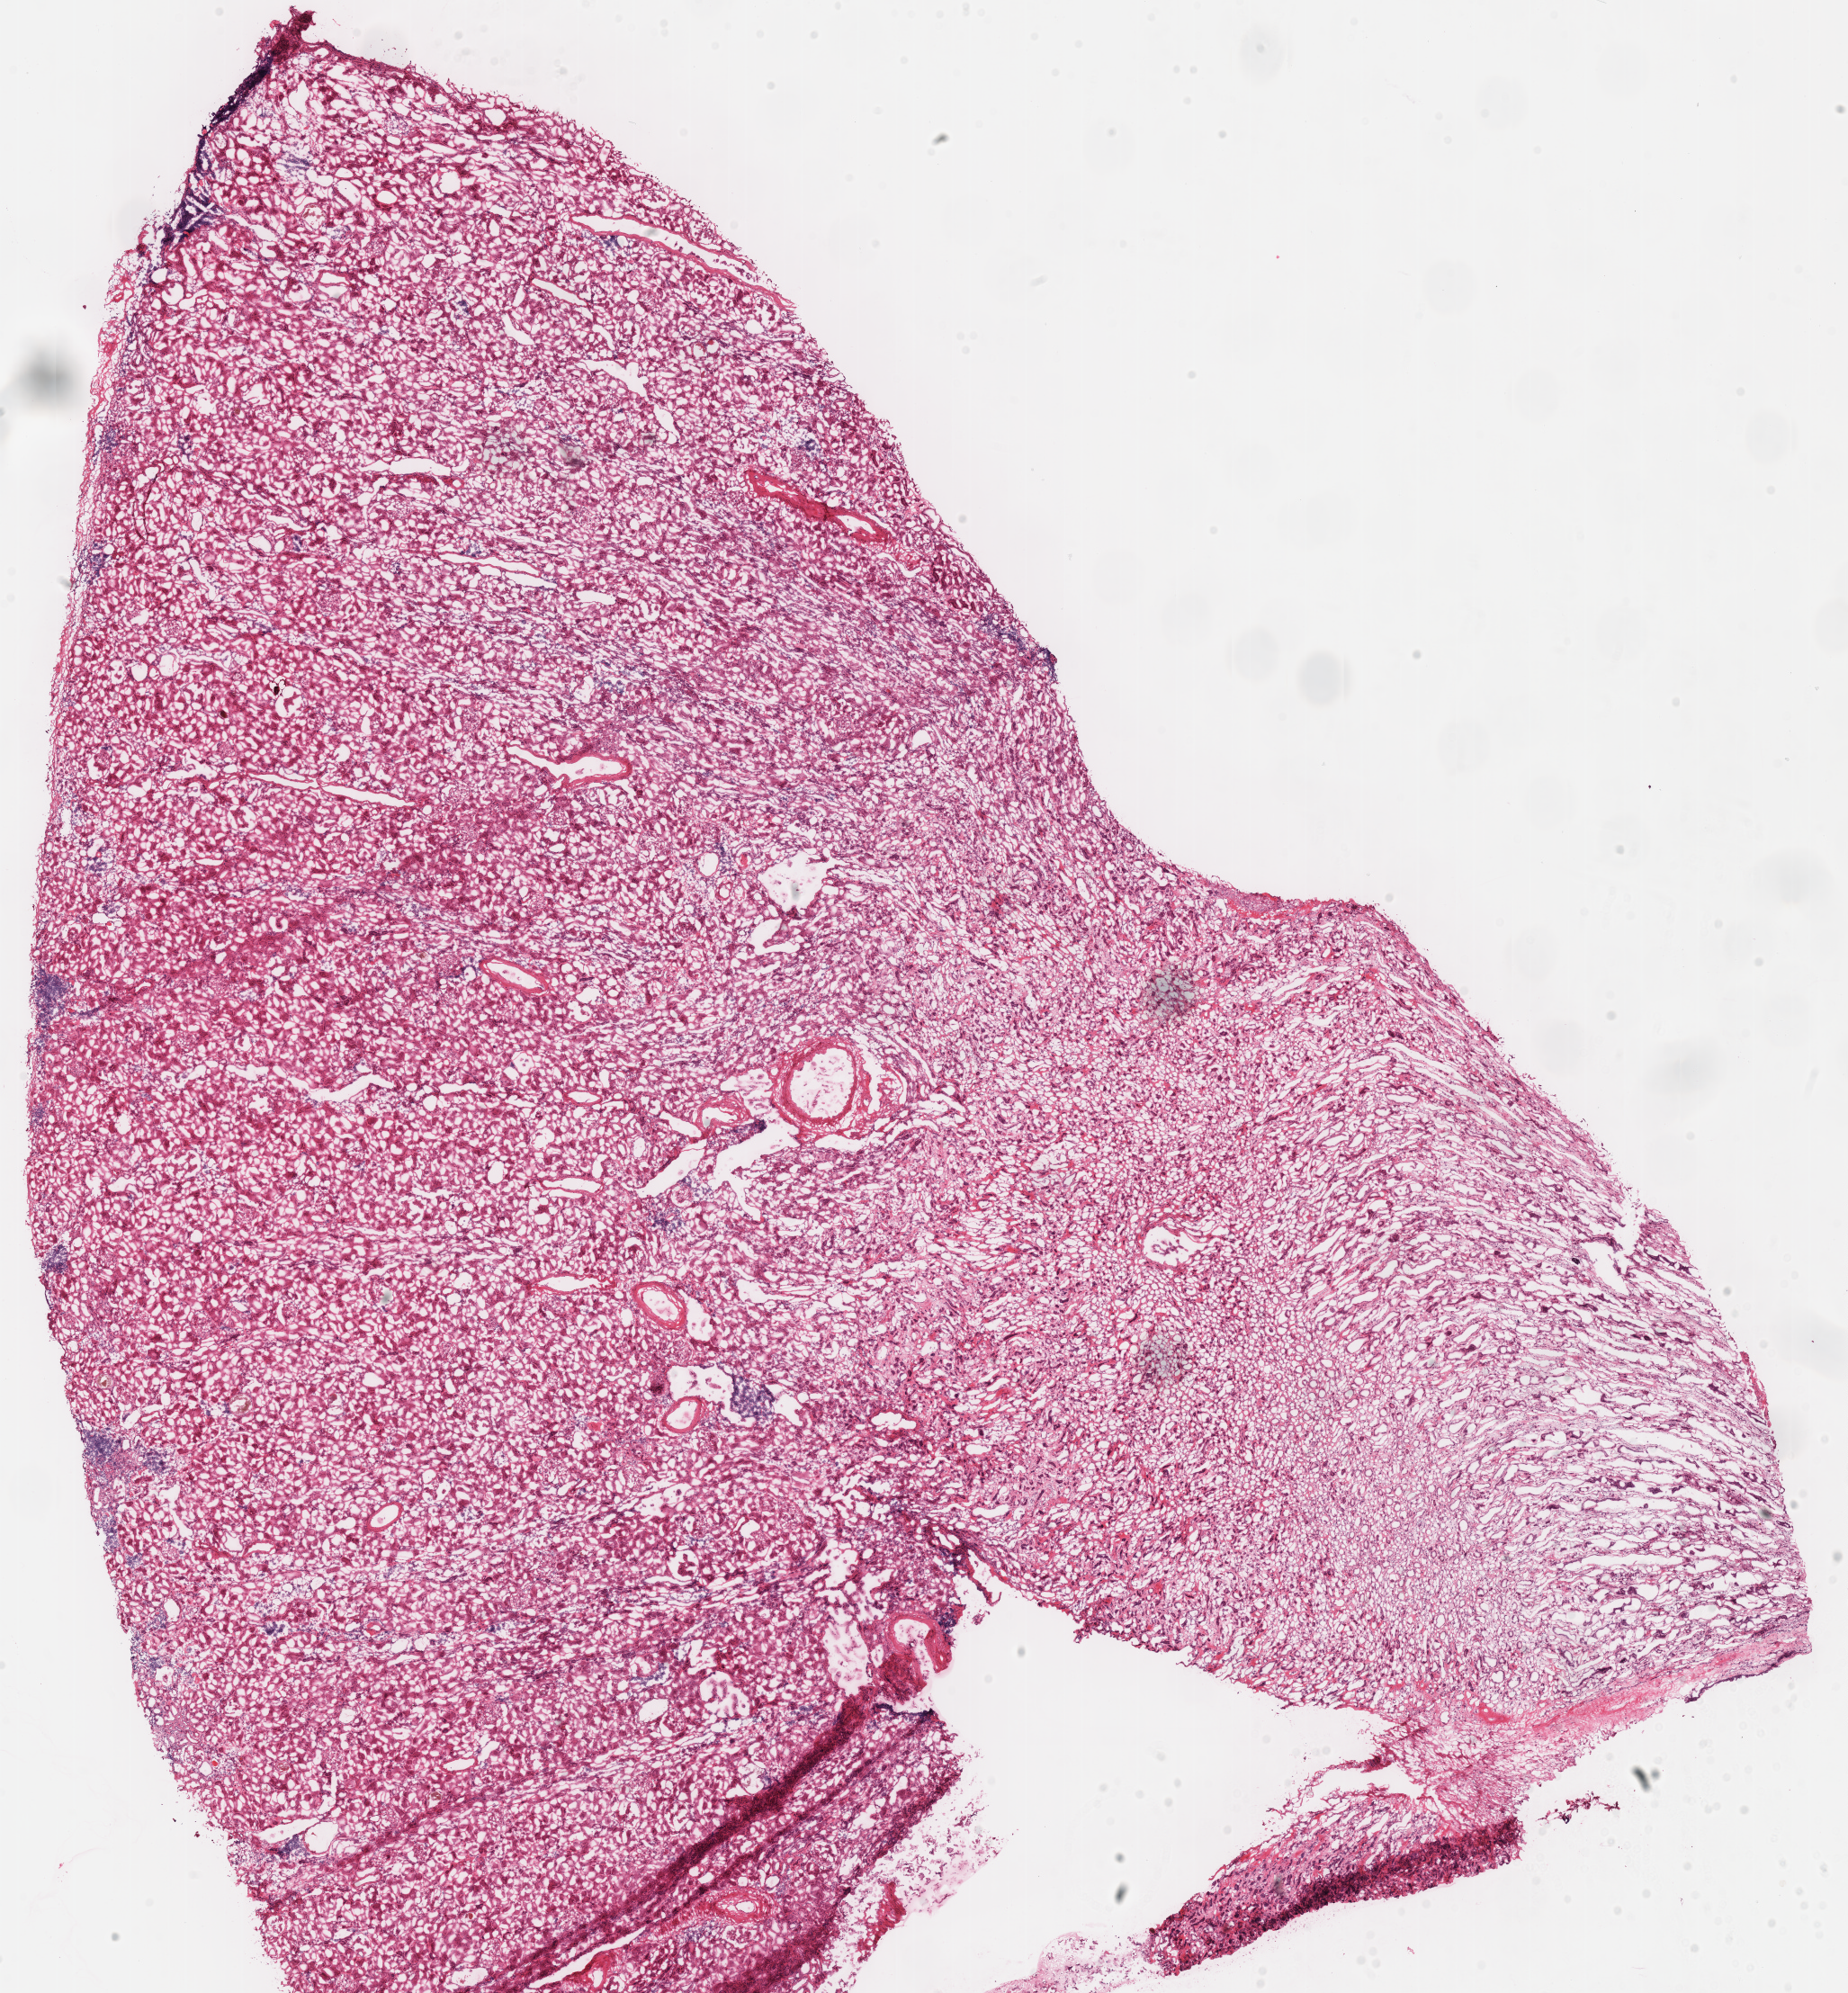
Digitized H&E tissue section (whole slide) — a low-resolution overview of the entire scanned area, about 16.2 x 17.4 mm (from a 40x scan), frozen section from the top of the tissue portion, solid tissue normal (non-tumour tissue) sample from the kidney. Male patient; age at initial diagnosis 69 years. Infiltration values recorded for this section: lymphocyte infiltration 4%, monocyte infiltration 0%, neutrophil infiltration 0%.
* this section: solid tissue normal sample (biorepository sample class)
* patient diagnosis: Renal cell carcinoma, chromophobe type